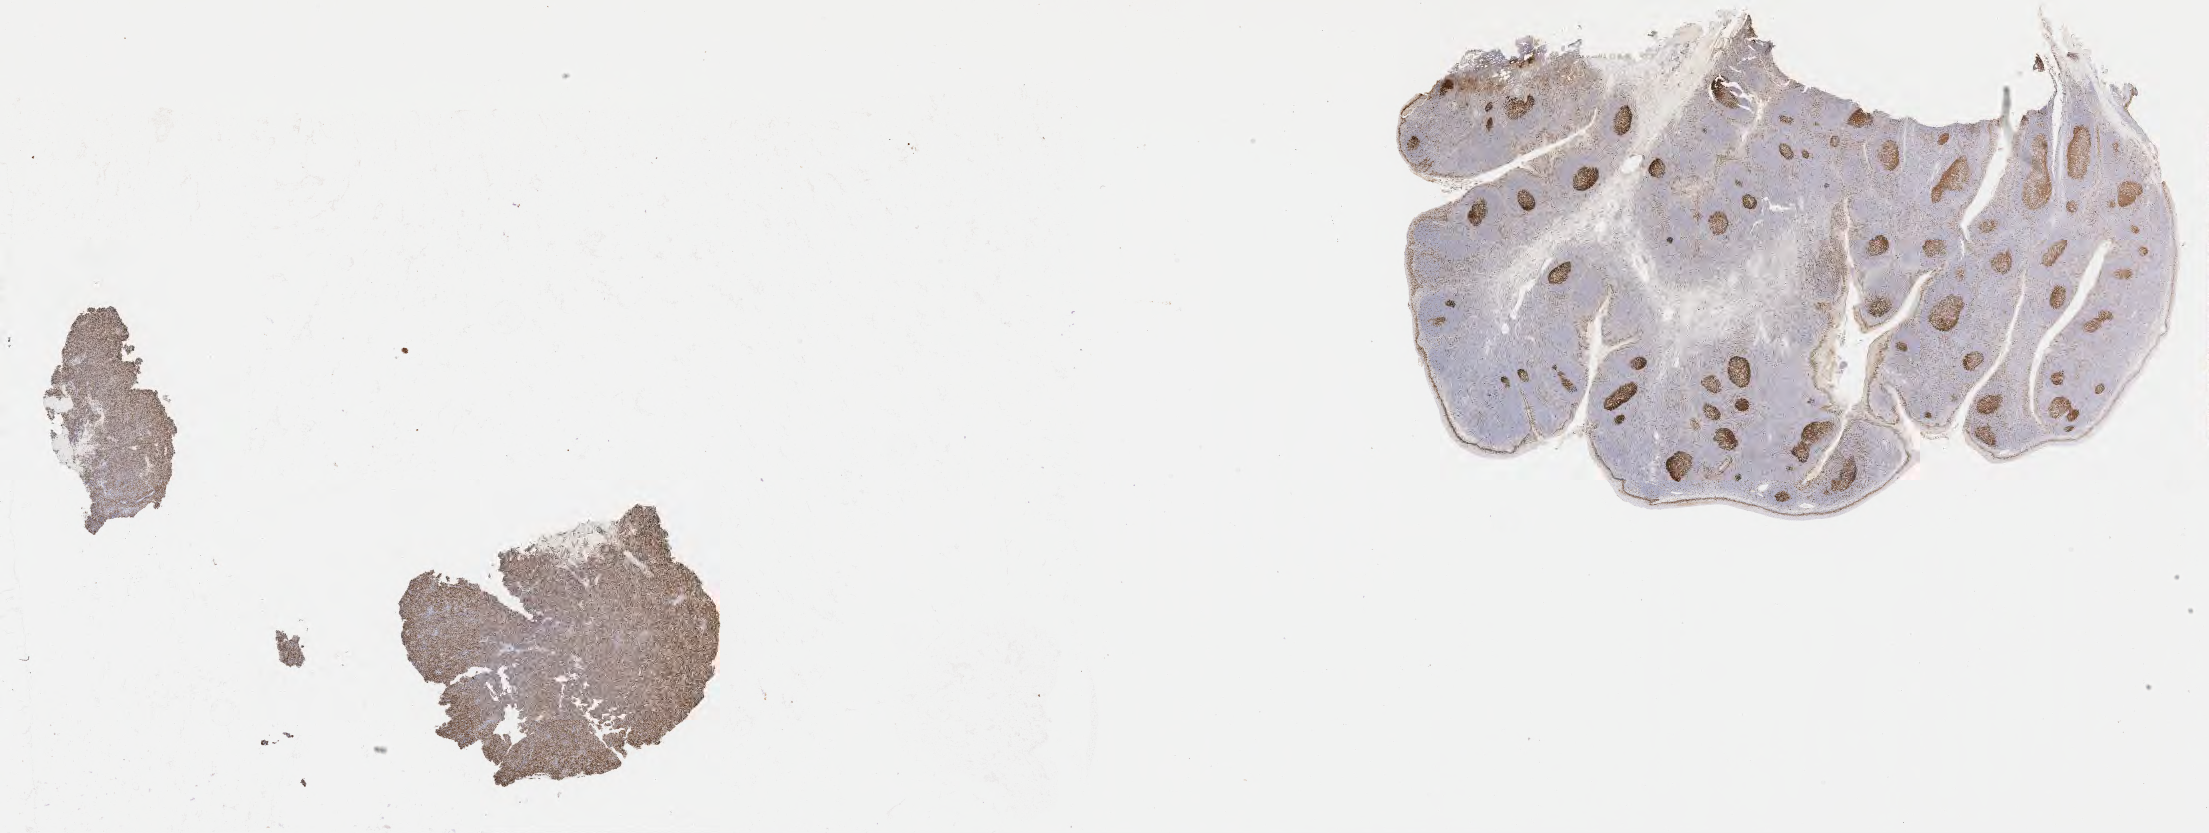
Whole-slide image, immunohistochemical stain for Ki-67, a low-resolution overview of the entire scanned area, about 35.7 x 13.5 mm, specimen: tumor tissue, site: lymph node. Female patient, 51 years old.
- histologic diagnosis: Diffuse large B-cell lymphoma, NOS